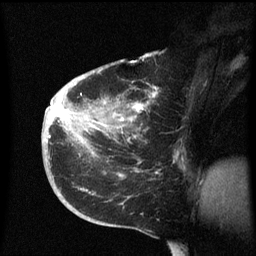
Breast MRI (dynamic contrast-enhanced), one sagittal slice; slice 31 of 60 in the series (ordered by position); dynamic contrast-enhanced series, image 2 of 3 at this slice position (ordered by acquisition); 1.5 T; TE 4.2 ms, TR 8.4 ms; 2.3 mm slice thickness; 256 × 256 image matrix. Female patient, age 38 years. Case-level facts recorded for this patient, not image findings: setting: breast cancer imaged before/during neoadjuvant chemotherapy; receptor status: HER2-positive.
Outlined on this slice (semi-automatic segmentation, software-assisted and operator-edited):
- analysis volume of interest (the breast-tissue region the enhancement analysis was run in; not a lesion): bounding box <42,78,178,213> (left, top, right, bottom; pixels)
- tumour enhancement mask (voxels above the 70 % enhancement threshold inside the analysis volume of interest): <50,104,143,137>